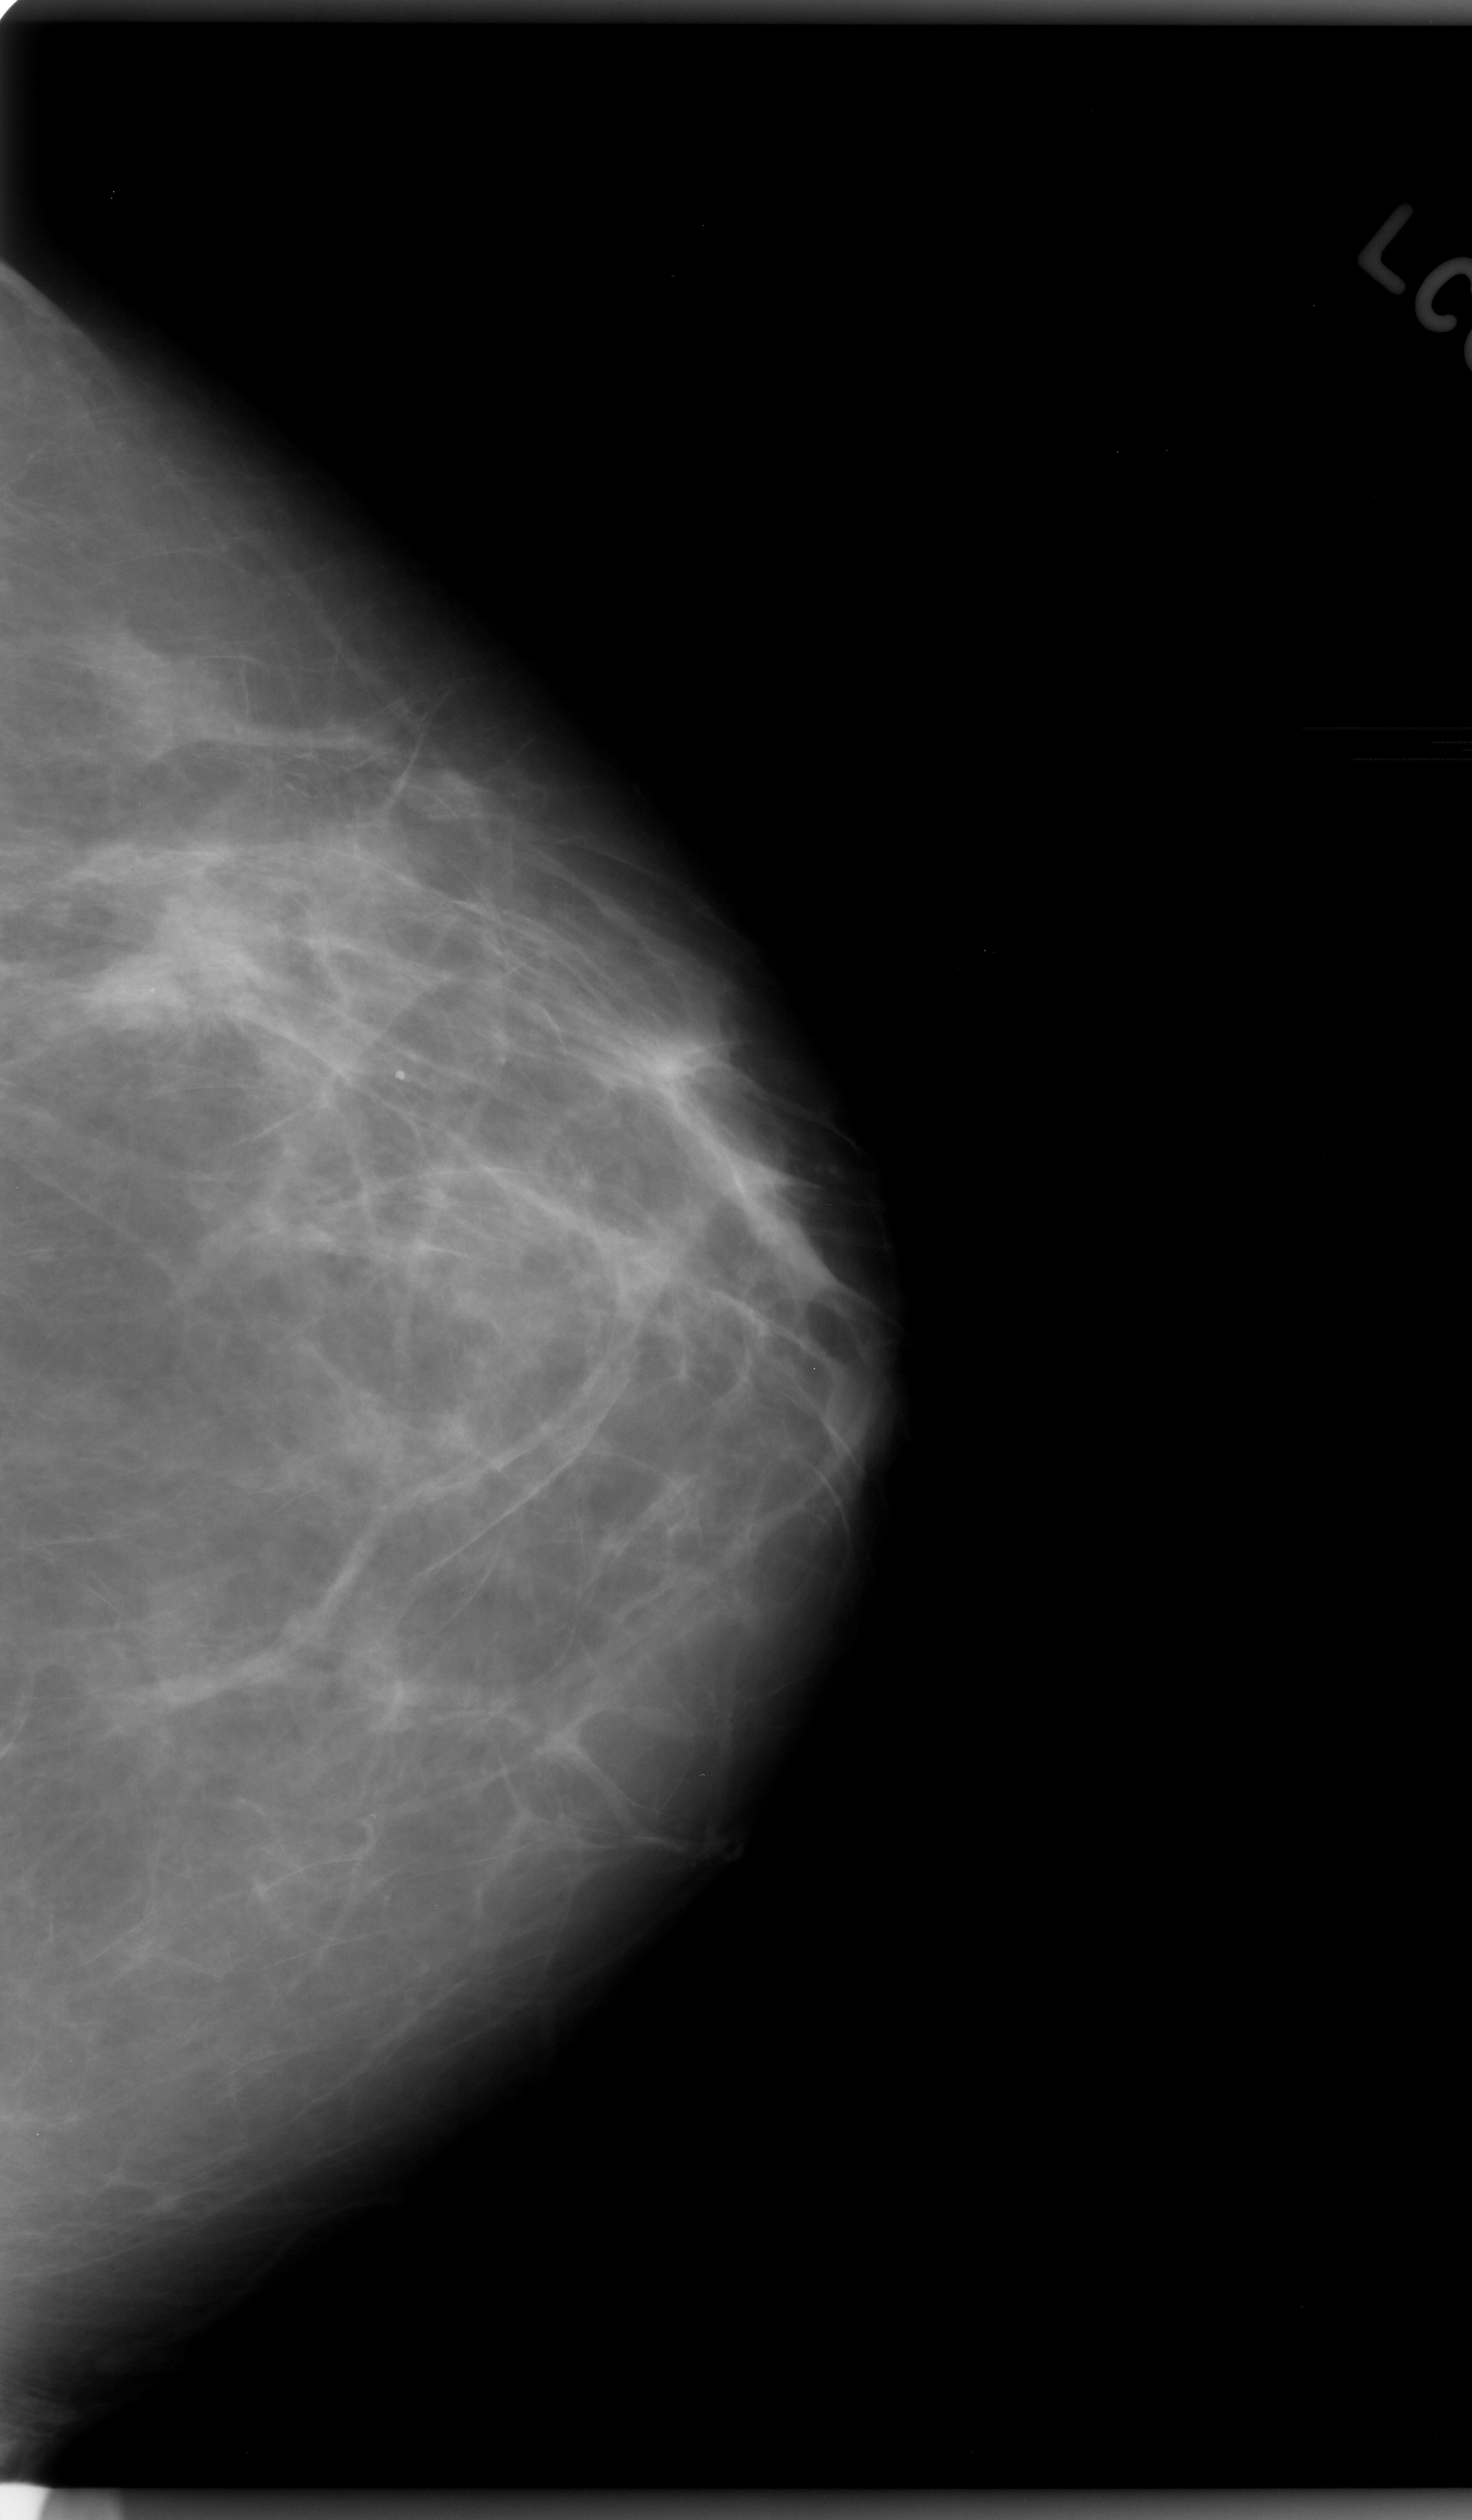
Mammogram (digitized film), left breast, CC view, breast composition: almost entirely fatty (BI-RADS density category 1 of 4).
Radiologist-marked abnormalities on this image: mass, shape irregular, margins ill defined; BI-RADS assessment category 5; subtlety rating 4 on a 1 (subtle) to 5 (obvious) scale; pathology result (as recorded, not read from the image): malignant.